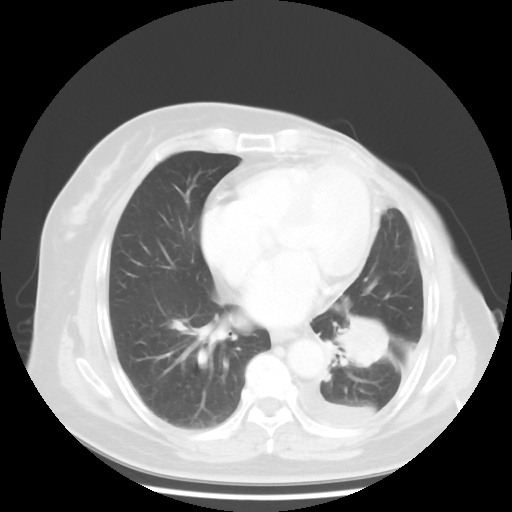
Chest CT, one axial slice; slice 18 of 48 in the series (ordered by position); lung window (W 1500 / L -600 HU); 512 × 512 image matrix, field of view 360 × 360 mm. Female patient, age 63 years. From the clinical record (not read from this slice): clinical TNM (as recorded): T2 N0 M1.
Annotated regions visible in this slice (rectangle marked by the reading radiologist):
- lung tumour (recorded histology: adenocarcinoma): bounding box [x1, y1, x2, y2] px = [325, 309, 390, 374]